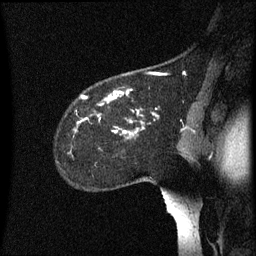
Breast MRI (dynamic contrast-enhanced), one sagittal slice. Slice 46 of 60 in the series (ordered by position). Dynamic contrast-enhanced series, image 2 of 3 at this slice position (ordered by acquisition). 1.5 T. TE 4.2 ms, TR 8.4 ms. 2.2 mm slice thickness. 256 × 256 image matrix. Patient: female, 35 years. From the clinical record (not read from this slice): setting: breast cancer imaged before/during neoadjuvant chemotherapy; receptor status: HER2-positive.
Outlined on this slice (semi-automatic segmentation, software-assisted and operator-edited):
- analysis volume of interest (the breast-tissue region the enhancement analysis was run in; not a lesion): bounding box [x1, y1, x2, y2] px = [57, 72, 159, 167]
- tumour enhancement mask (voxels above the 70 % enhancement threshold inside the analysis volume of interest): [82, 90, 145, 135]